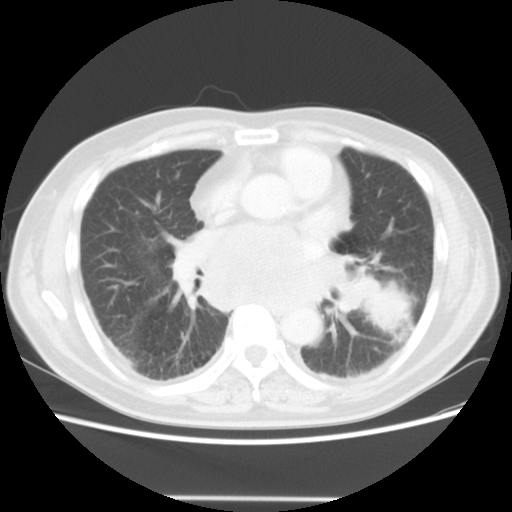
Chest CT, one axial slice. Position 25 of 56 along the scan axis. Reconstruction kernel STANDARD. Lung window (W 1500 / L -600 HU). 512 × 512 image matrix, field of view 360 × 360 mm. Patient: male, 66 years. Case-level facts recorded for this patient, not image findings: clinical TNM (as recorded): T4 N3 M0.
Annotated regions visible in this slice (rectangle marked by the reading radiologist):
- lung tumour (recorded histology: small cell carcinoma): box from (x=355, y=282) to (x=407, y=338) px